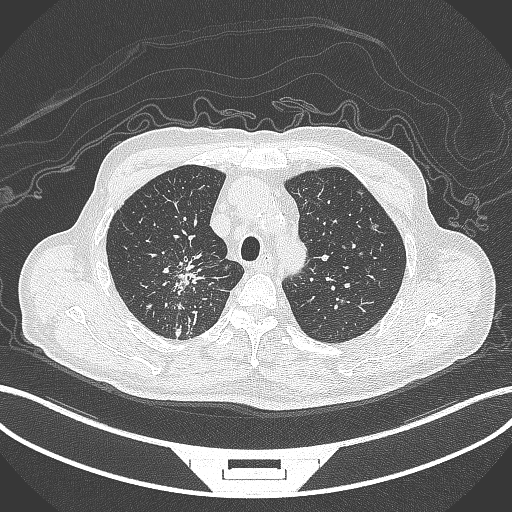
Chest CT, one axial slice. Slice 296 of 407 in the series (ordered by position). 120 kVp. Lung window (W 1500 / L -600 HU). 1 mm slice thickness. 512 × 512 image matrix, field of view 400 × 400 mm. Male patient, age 69 years. From the clinical record (not read from this slice): clinical TNM (as recorded): T1c N1 M1.
Annotated regions visible in this slice (bounding box drawn by a radiologist):
- lung tumour (recorded histology: adenocarcinoma): box from (x=160, y=249) to (x=212, y=303) px